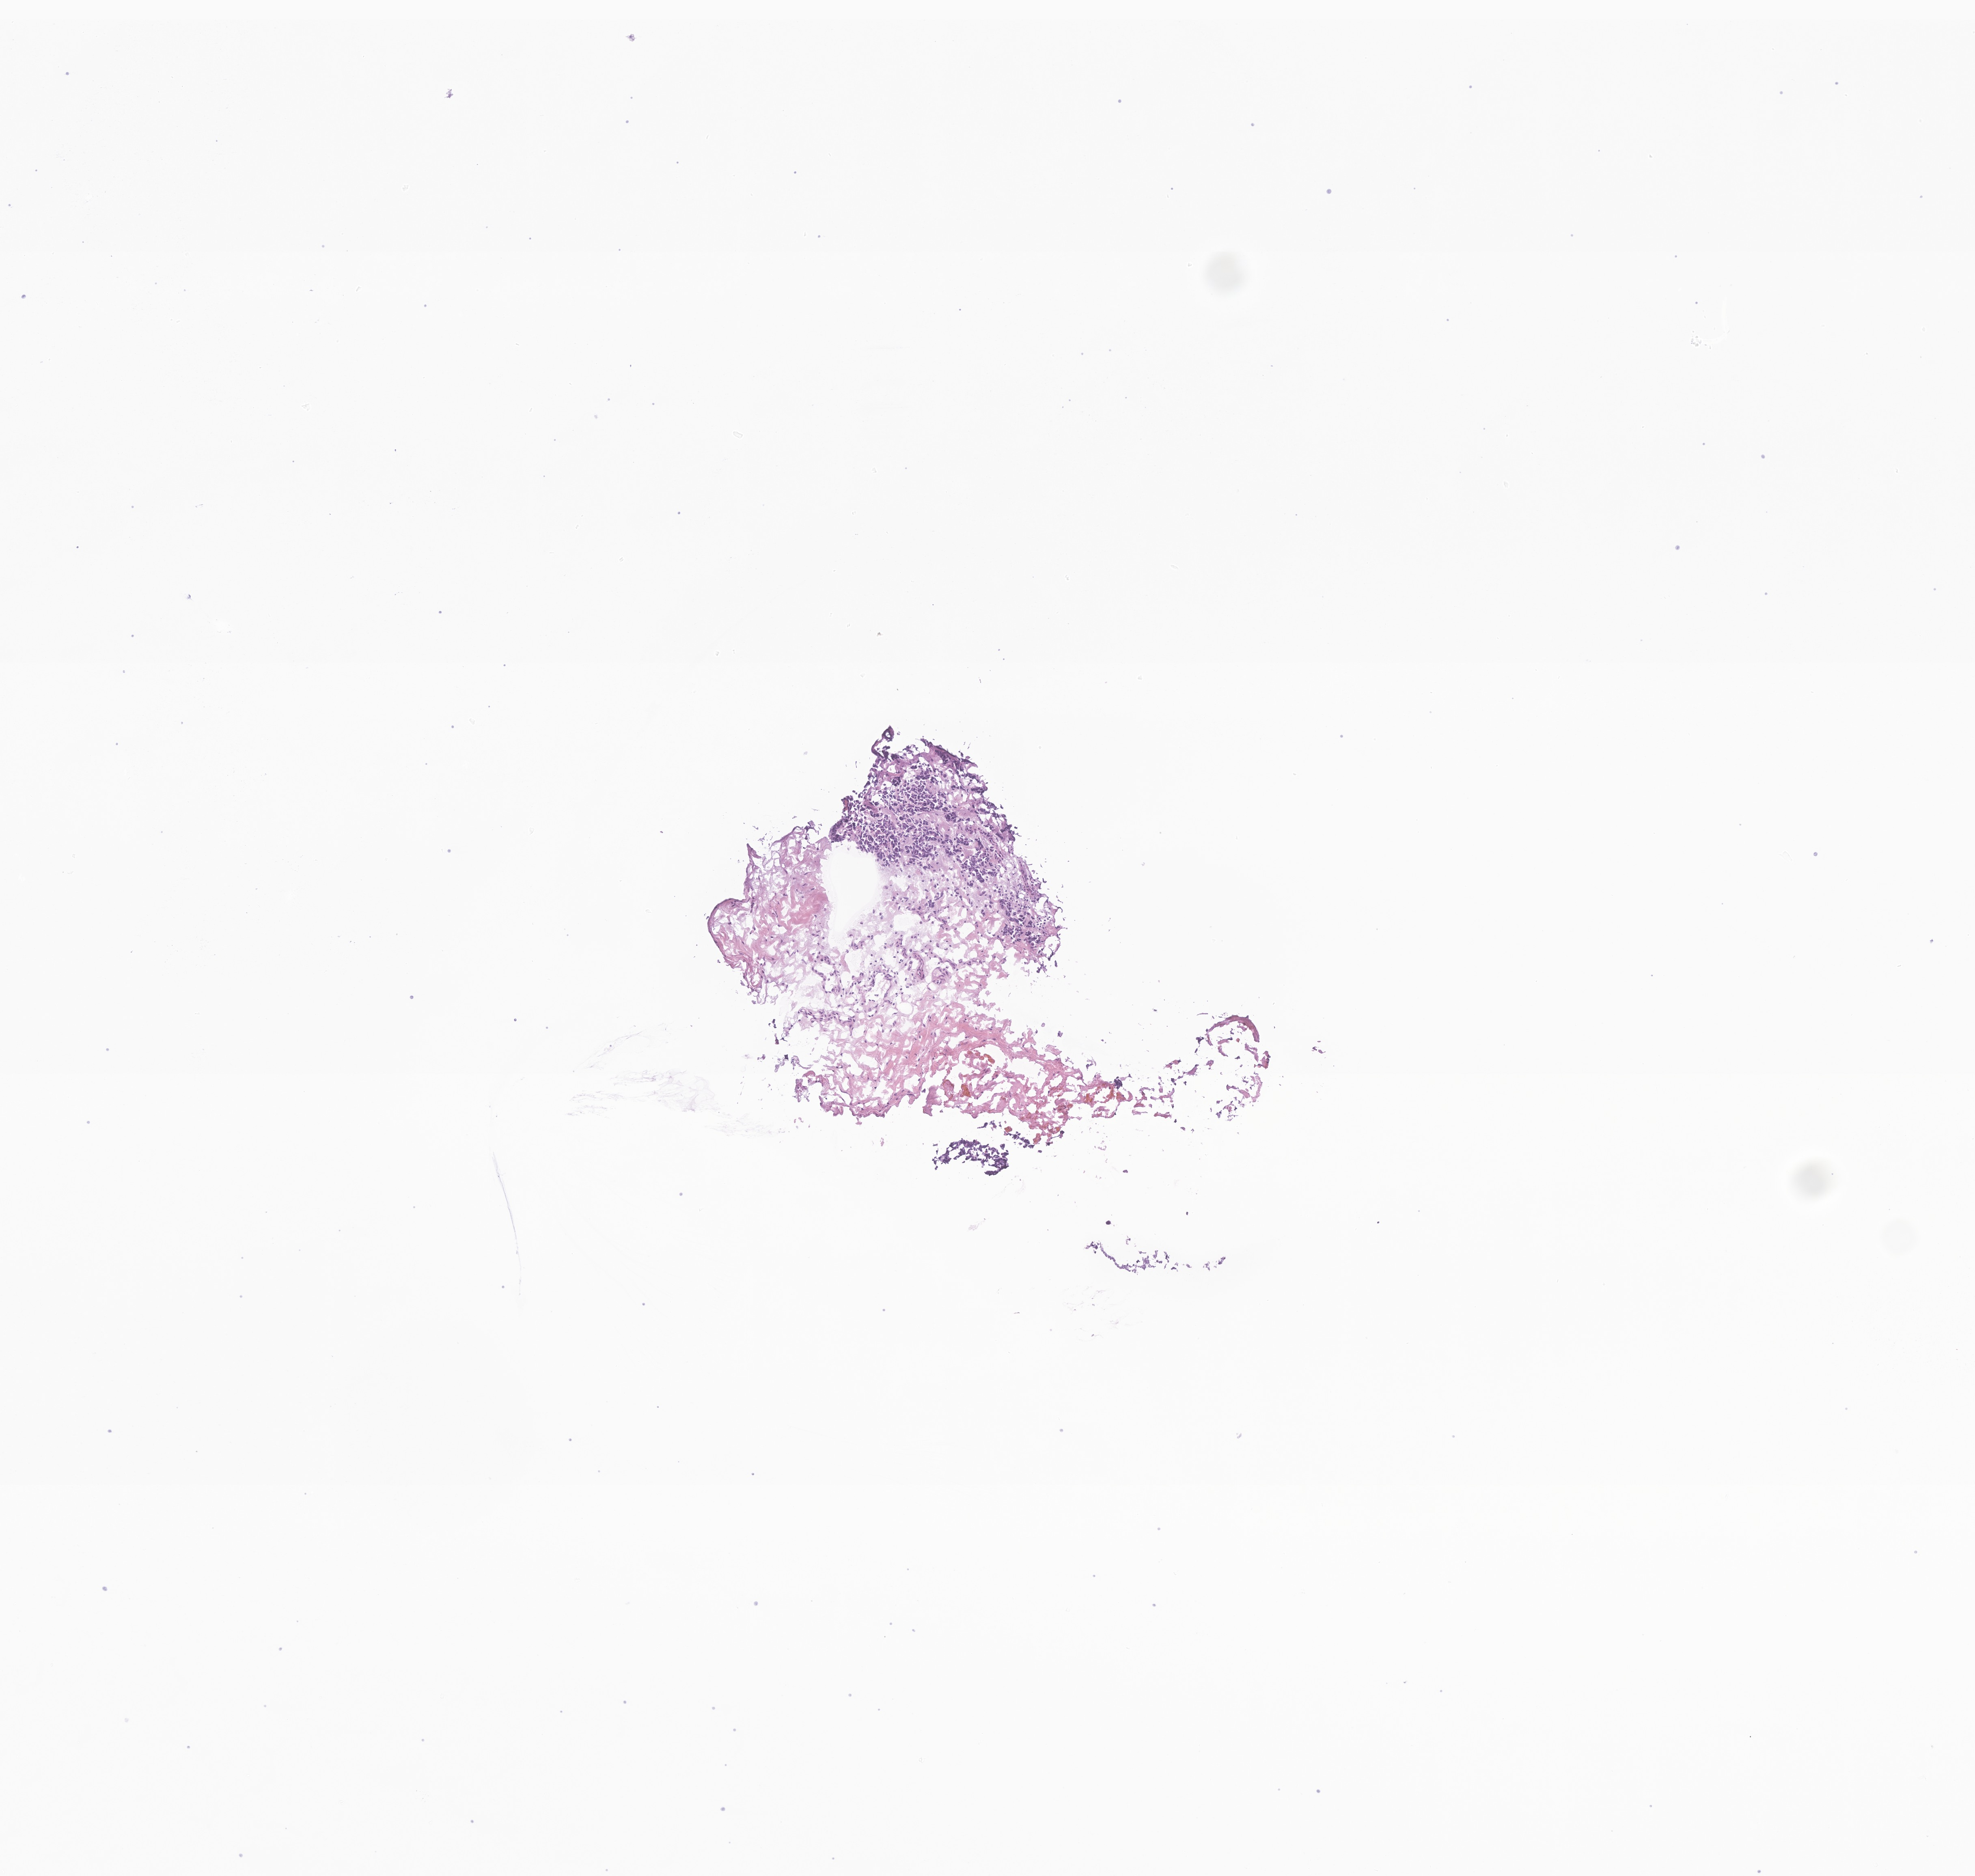
Digitized H&E-stained section of tumor tissue from the soft tissue of upper extremity, whole scanned area (about 5.1 x 4.9 mm) shown as a low-resolution overview. Frozen section (OCT-embedded). Patient: female, age 91 months (7 years 7 months).
Tissue or organ of origin (case record): connective, subcutaneous and other soft tissues of upper limb and shoulder. Diagnosis: Alveolar rhabdomyosarcoma.